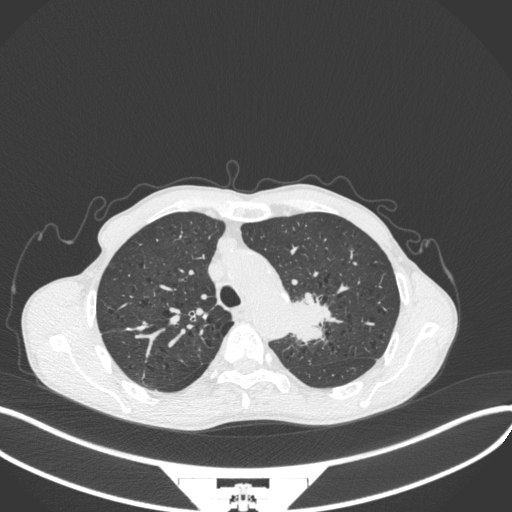
Chest CT, one axial slice; slice 313 of 394 in the series (ordered by position); reconstruction kernel B31f; 120 kVp; lung window (W 1500 / L -600 HU); 512 × 512 image matrix, field of view 400 × 400 mm. Patient: male, 65 years. From the clinical record (not read from this slice): clinical TNM (as recorded): T2b N0 M0; histopathological grade: G2.
Outlined on this slice (bounding box drawn by a radiologist):
- lung tumour (recorded histology: adenocarcinoma): bounding box [x1, y1, x2, y2] px = [290, 286, 337, 345]